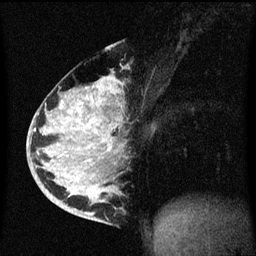
Breast MRI (dynamic contrast-enhanced), one sagittal slice; position 31 of 60 along the scan axis; dynamic contrast-enhanced series, image 2 of 3 at this slice position (ordered by acquisition); 1.5 T; TE 4.2 ms, TR 8.4 ms; 2 mm slice thickness; 256 × 256 image matrix, field of view 200 × 200 mm. Female patient, age 34 years. Case-level facts recorded for this patient, not image findings: setting: breast cancer imaged before/during neoadjuvant chemotherapy; receptor status: HR-positive, HER2-negative.
Outlined on this slice (semi-automatically segmented with operator editing):
- analysis volume of interest (the breast-tissue region the enhancement analysis was run in; not a lesion): bounding box [x1, y1, x2, y2] px = [34, 48, 125, 215]
- tumour enhancement mask (voxels above the 70 % enhancement threshold inside the analysis volume of interest): [52, 82, 113, 215]